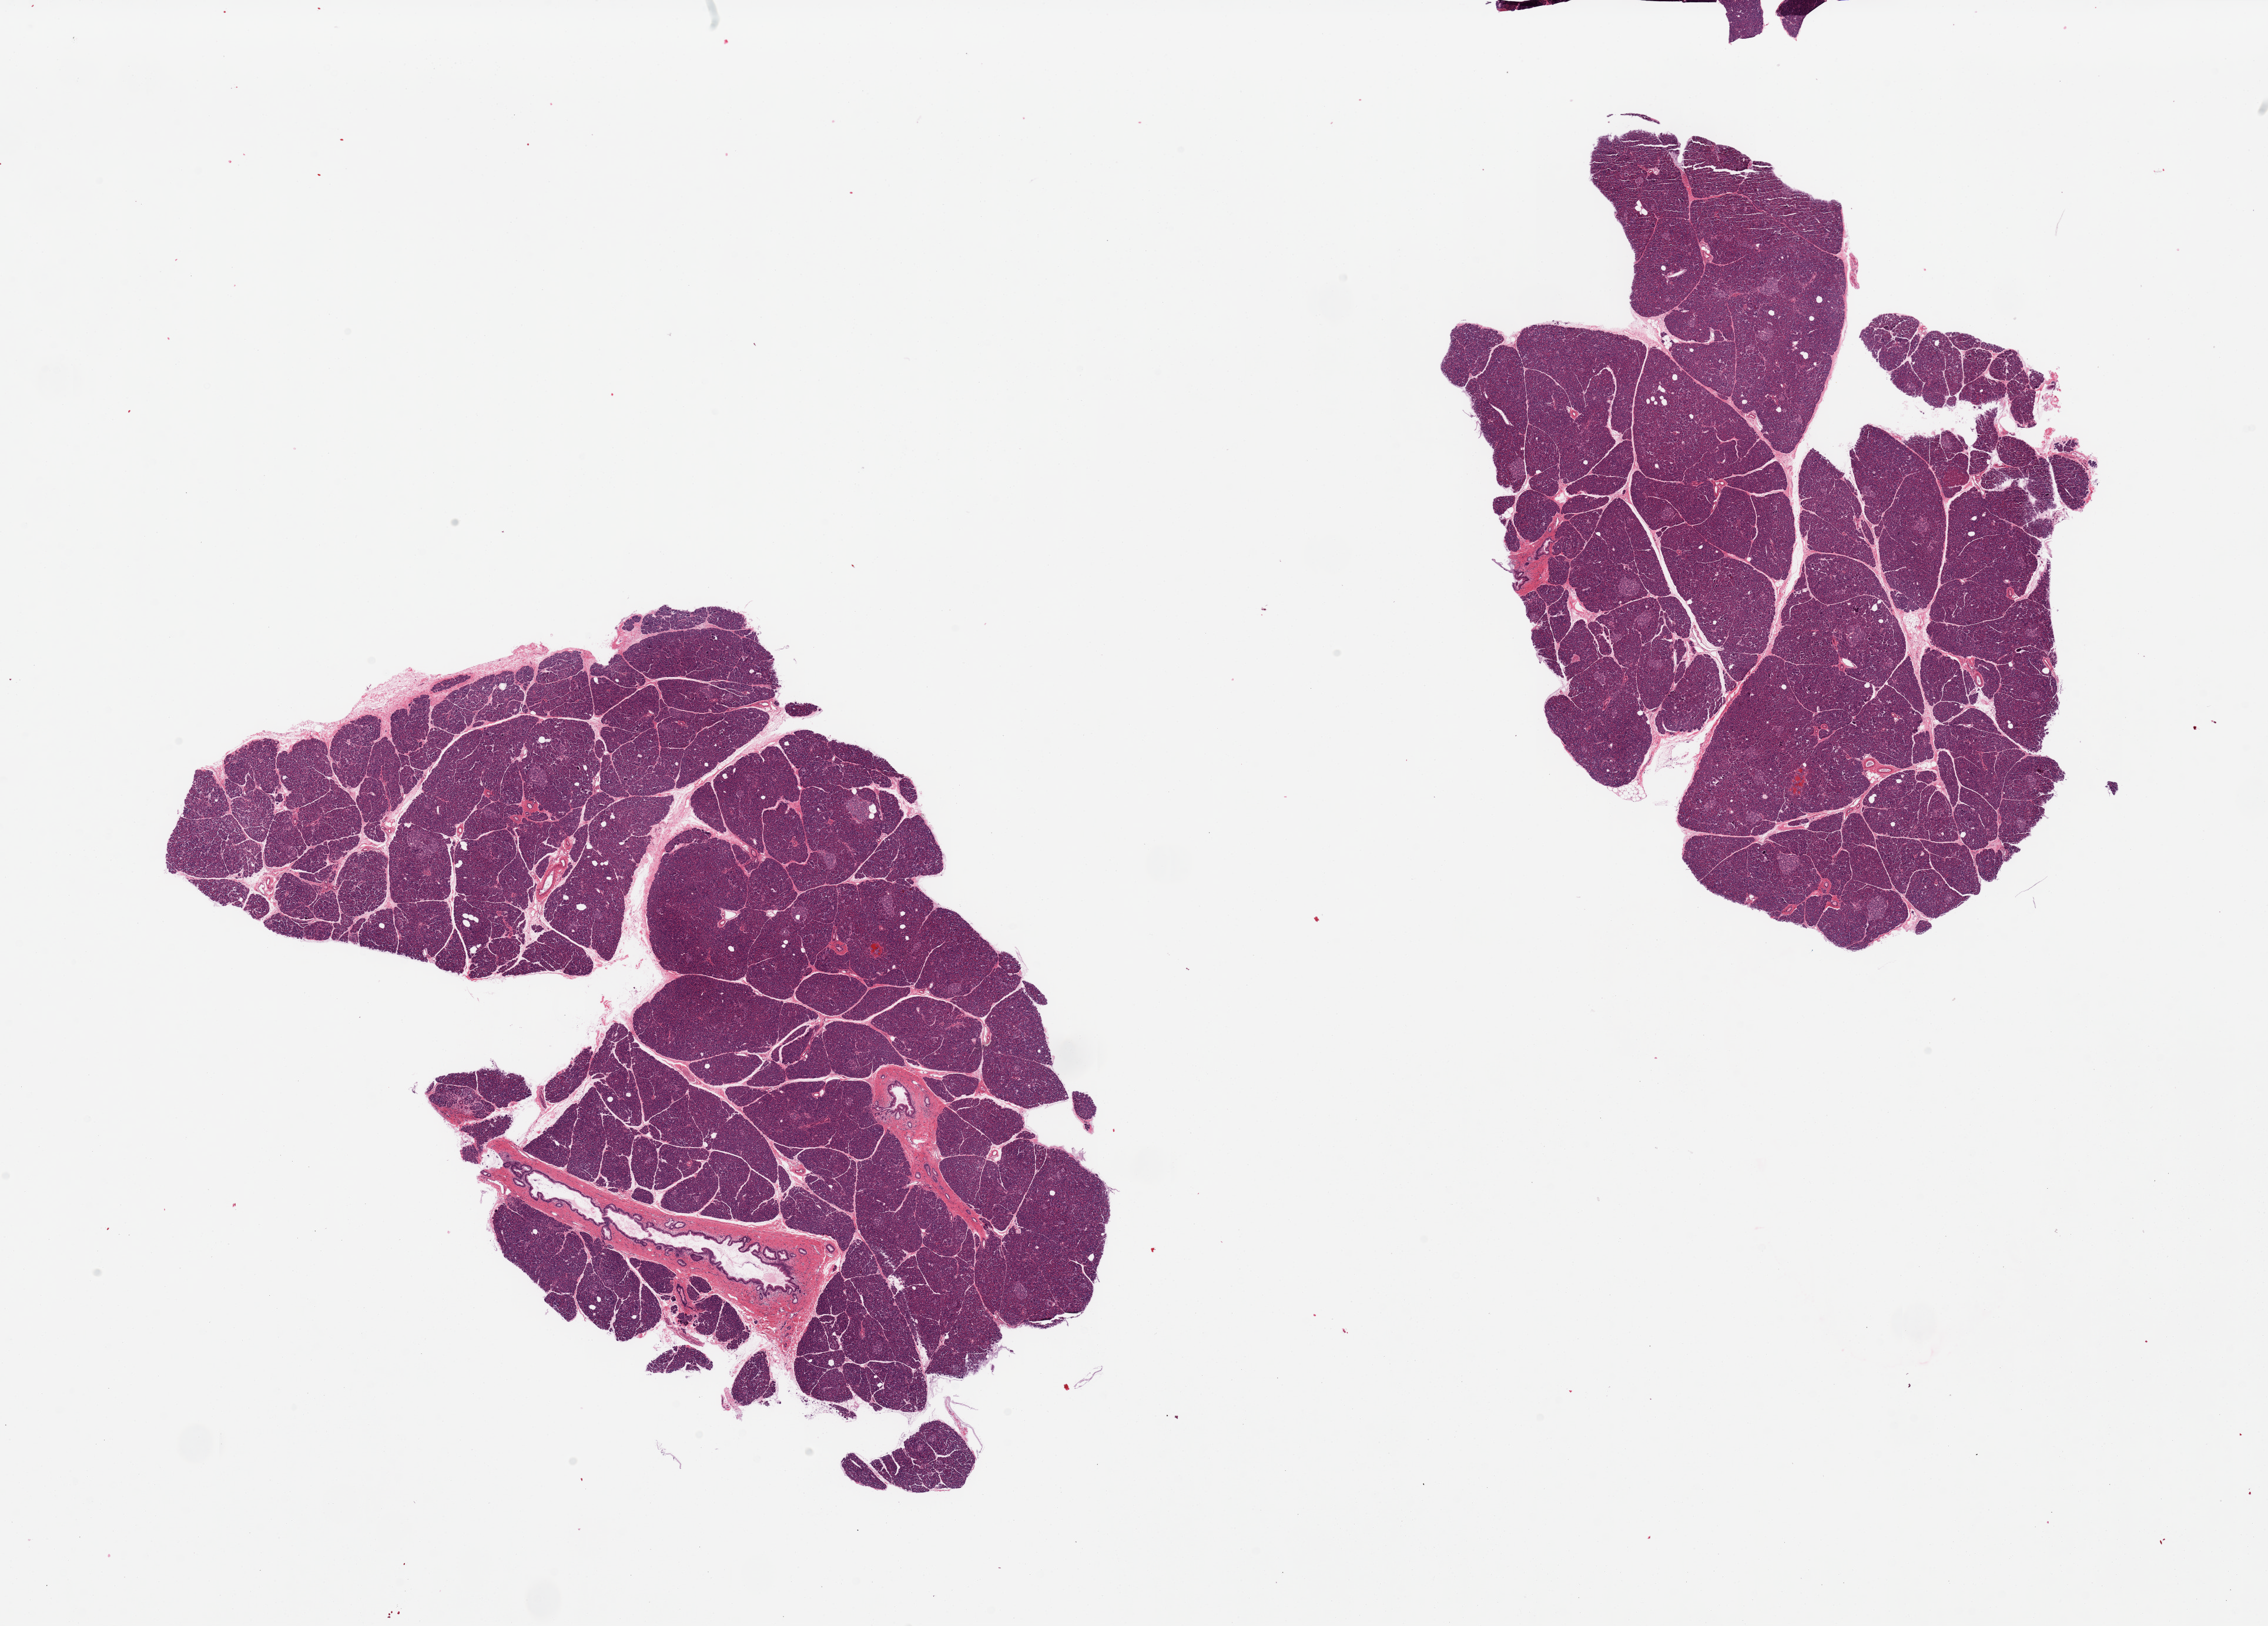
Digitized hematoxylin and eosin (H&E)-stained section — a low-resolution overview of the entire scanned area, about 30.5 x 21.9 mm; PAXgene-fixed paraffin-embedded (PFPE) section; sampled site (target tissue): pancreas; tissue donor sample. Donor: male.
Review note (as recorded): 2 pieces.